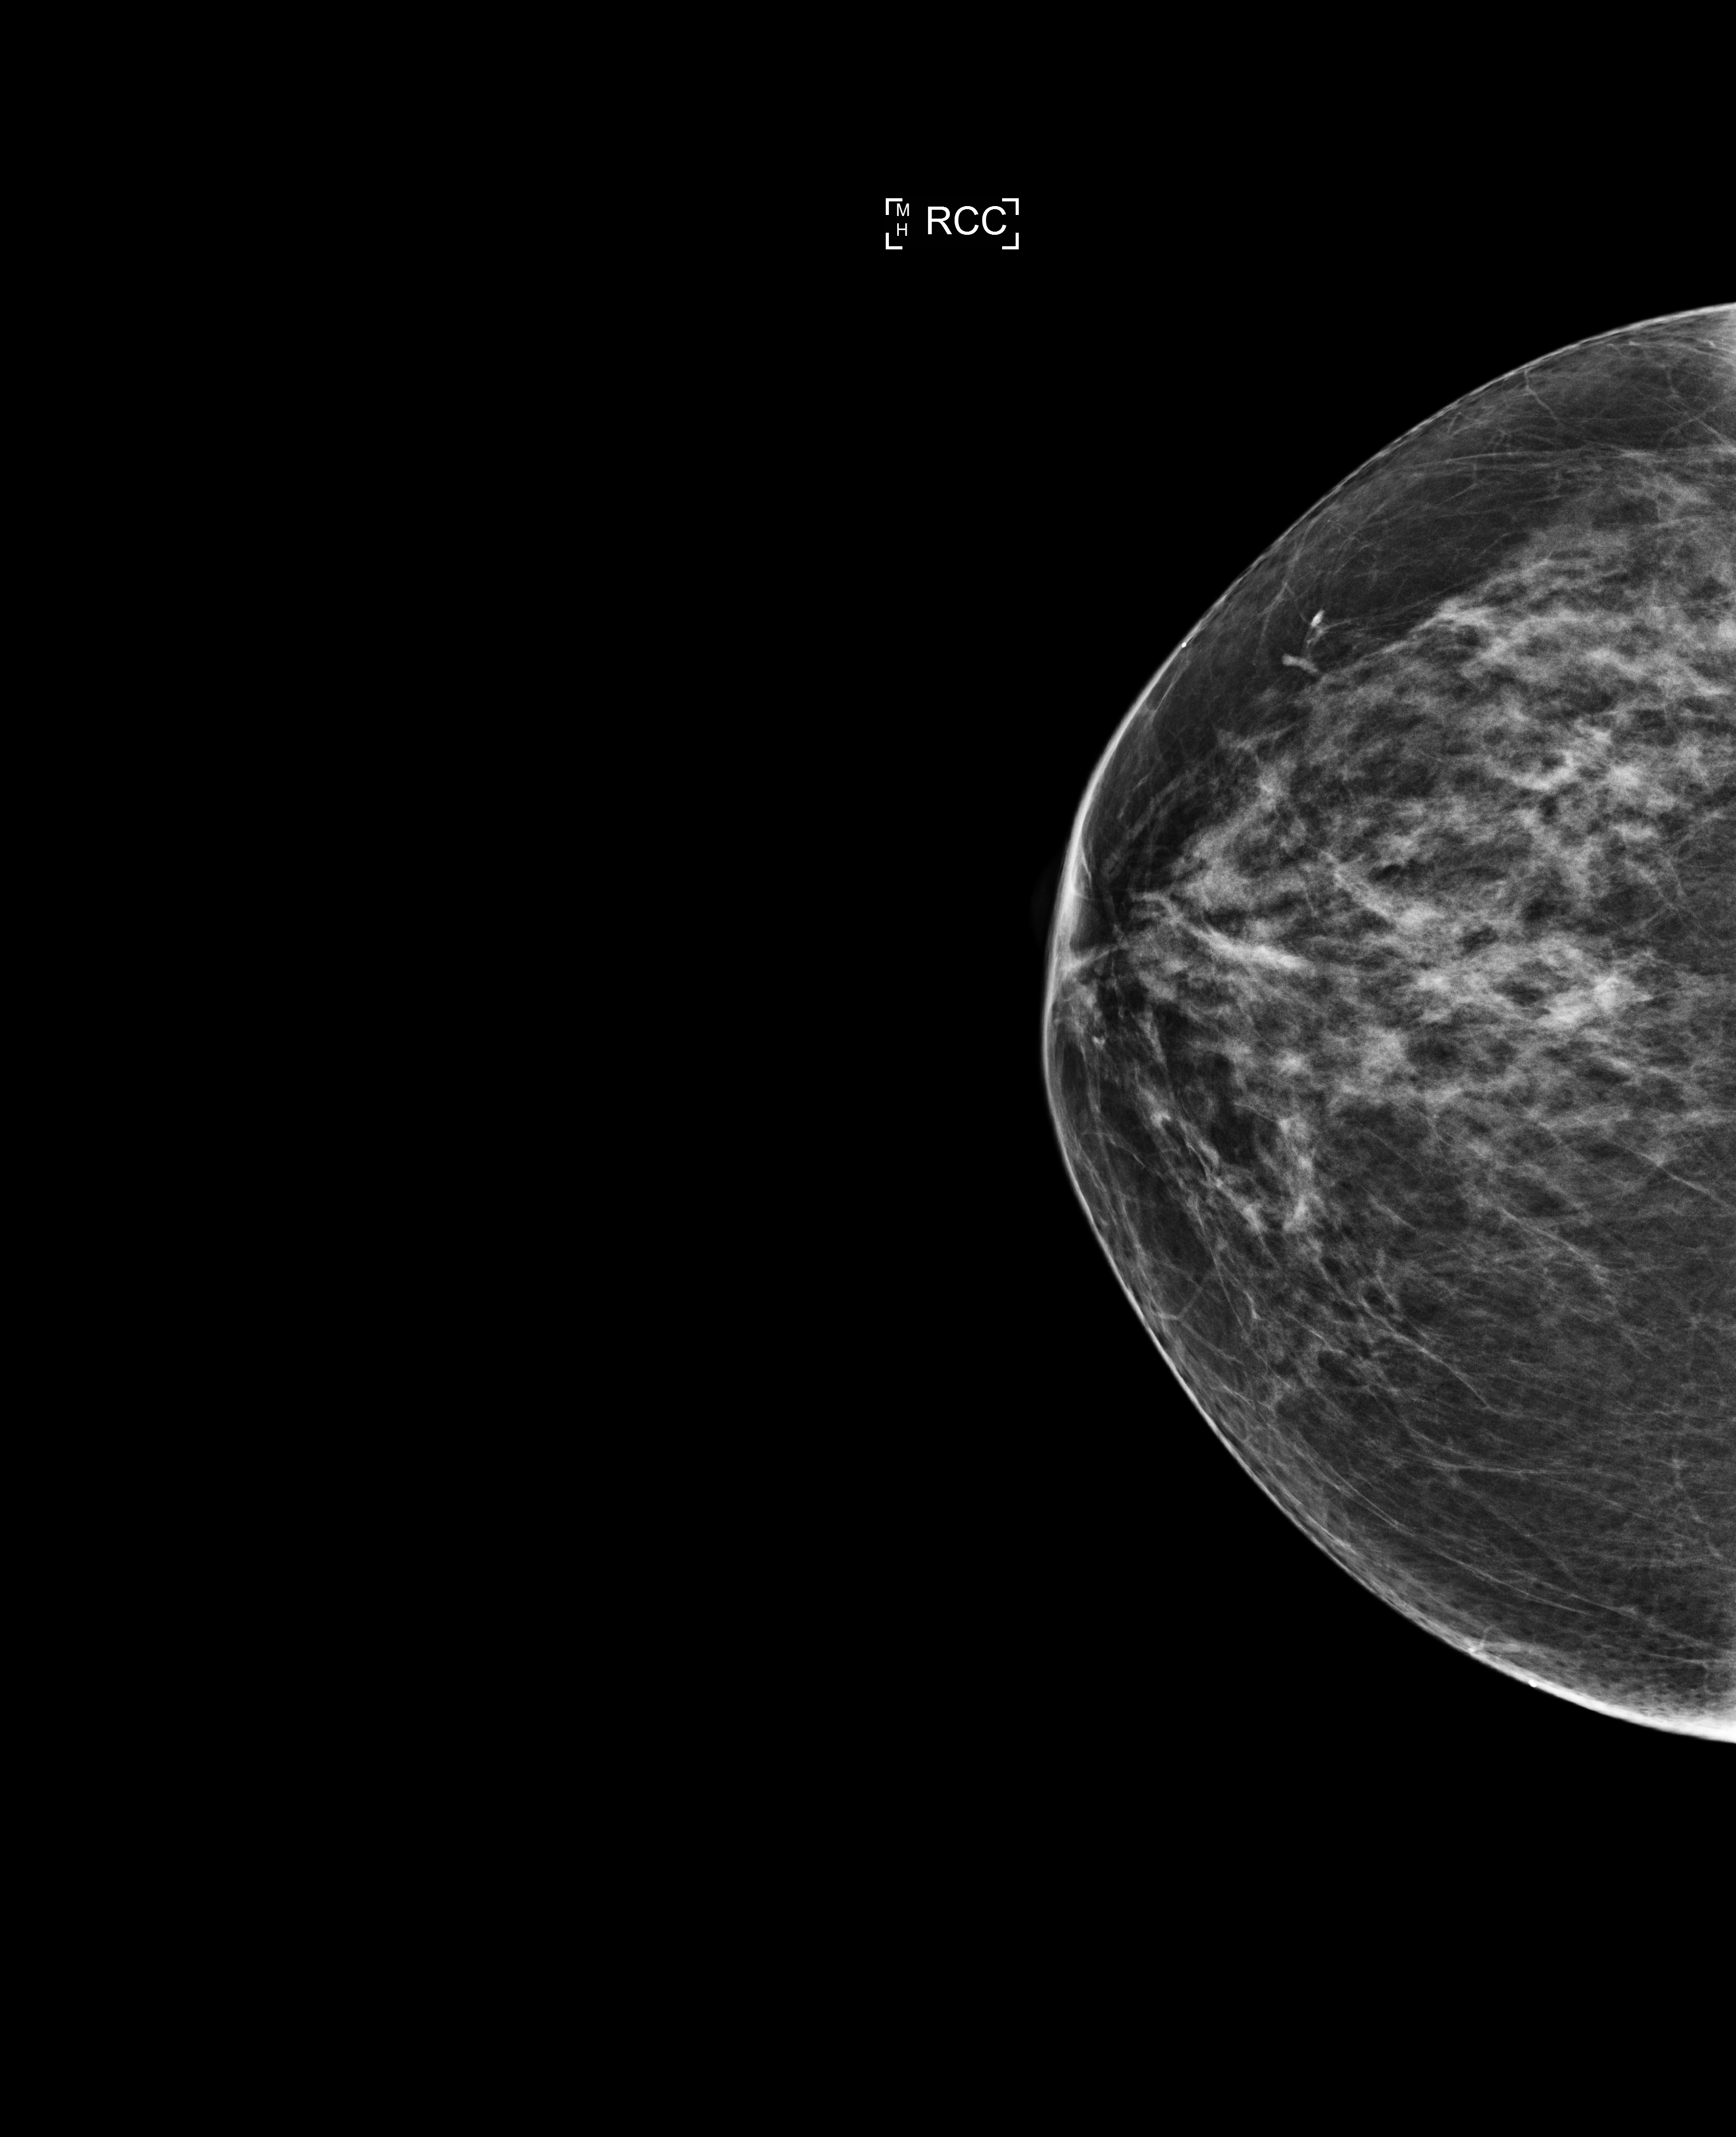
Annual screening mammography examination. Female patient, age 70 years.
Image type: full-field digital mammogram. Breast: right. Projection: craniocaudal (CC) view. BI-RADS breast density category at the screening exam (both breasts, scale 1–4): 2. Final BI-RADS assessment for this screening round (tomosynthesis exam, both breasts): category 1. Recall: no recall after this screen.